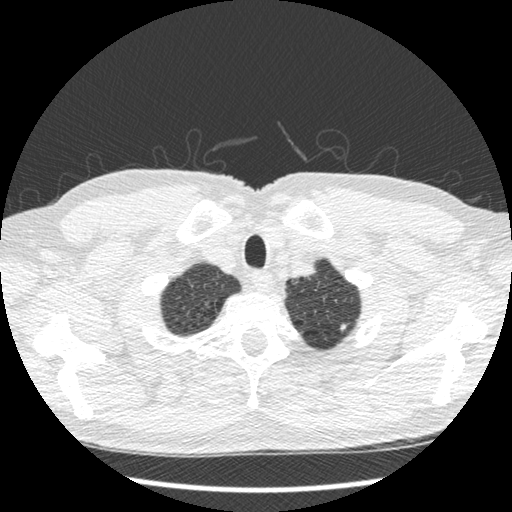
Low-dose screening chest CT, one axial slice; slice 413 of 439 in the series (ordered by position); reconstruction kernel STANDARD; lung window (W 1500 / L -600 HU); 512 × 512 image matrix.
Outlined on this slice (expert manual segmentation):
- lesion 1 (nodule, upper lobe of left lung): bounding box (x1, y1, x2, y2) in pixels: (340, 323, 348, 332)